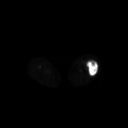
FDG PET of an extremity soft-tissue mass (from a PET/CT study), one axial slice; slice 208 of 267 in the series (ordered by position); 3.27 mm slice thickness; 128 × 128 image matrix, field of view 700 × 700 mm. Female patient, age 62 years. From the clinical record (not read from this slice): histological type: undifferentiated – high grade; grade: high; site of the primary tumour: left thigh.
Annotated regions visible in this slice (expert contour drawn on MRI and transferred to this co-registered scan by the dataset authors):
- gross tumour volume including surrounding oedema: bounding box (x1, y1, x2, y2) in pixels: (83, 59, 98, 75)
- gross tumour volume (mass): (86, 59, 98, 75)